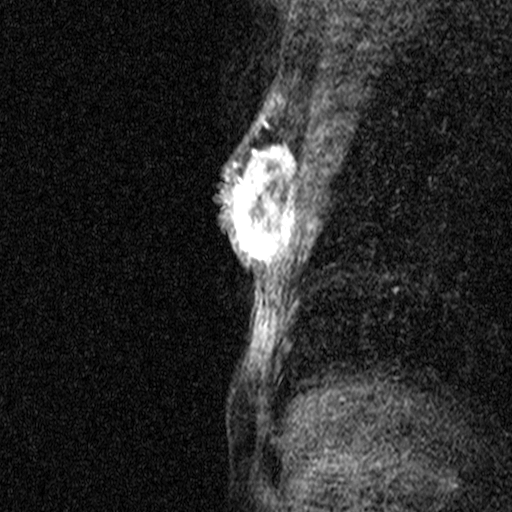
Breast MRI (dynamic contrast-enhanced), one sagittal slice; slice 28 of 44 in the series (ordered by position); dynamic contrast-enhanced study with each time point stored as its own series, time point 2 of 3 at this slice position (early post-contrast, ordered by acquisition time); 1.5 T; TE 4.5 ms, TR 11 ms; 512 × 512 image matrix, field of view 200 × 200 mm. Patient: female, 44 years. Case-level facts recorded for this patient, not image findings: setting: breast cancer imaged before/during neoadjuvant chemotherapy; receptor status: HR-positive, HER2-negative.
Annotated regions visible in this slice (semi-automatically segmented with operator editing):
- analysis volume of interest (the breast-tissue region the enhancement analysis was run in; not a lesion): bounding box <218,118,299,291> (left, top, right, bottom; pixels)
- tumour enhancement mask (voxels above the 90 % enhancement threshold inside the analysis volume of interest): <227,125,296,259>